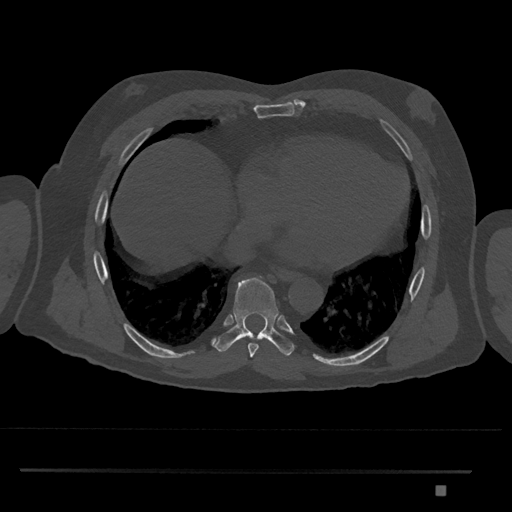
CT including the spine, one axial slice. Position 1125 of 1134 along the scan axis. Bone window (W 1800 / L 400 HU). 0.5 mm slice thickness. 512 × 512 image matrix, field of view 429 × 429 mm. Patient: male, 65 years. Case-level facts recorded for this patient, not image findings: primary cancer: prostate.
Outlined on this slice (semi-automatic segmentation, software-assisted and operator-edited):
- T8 vertebra: box from (x=214, y=276) to (x=295, y=357) px